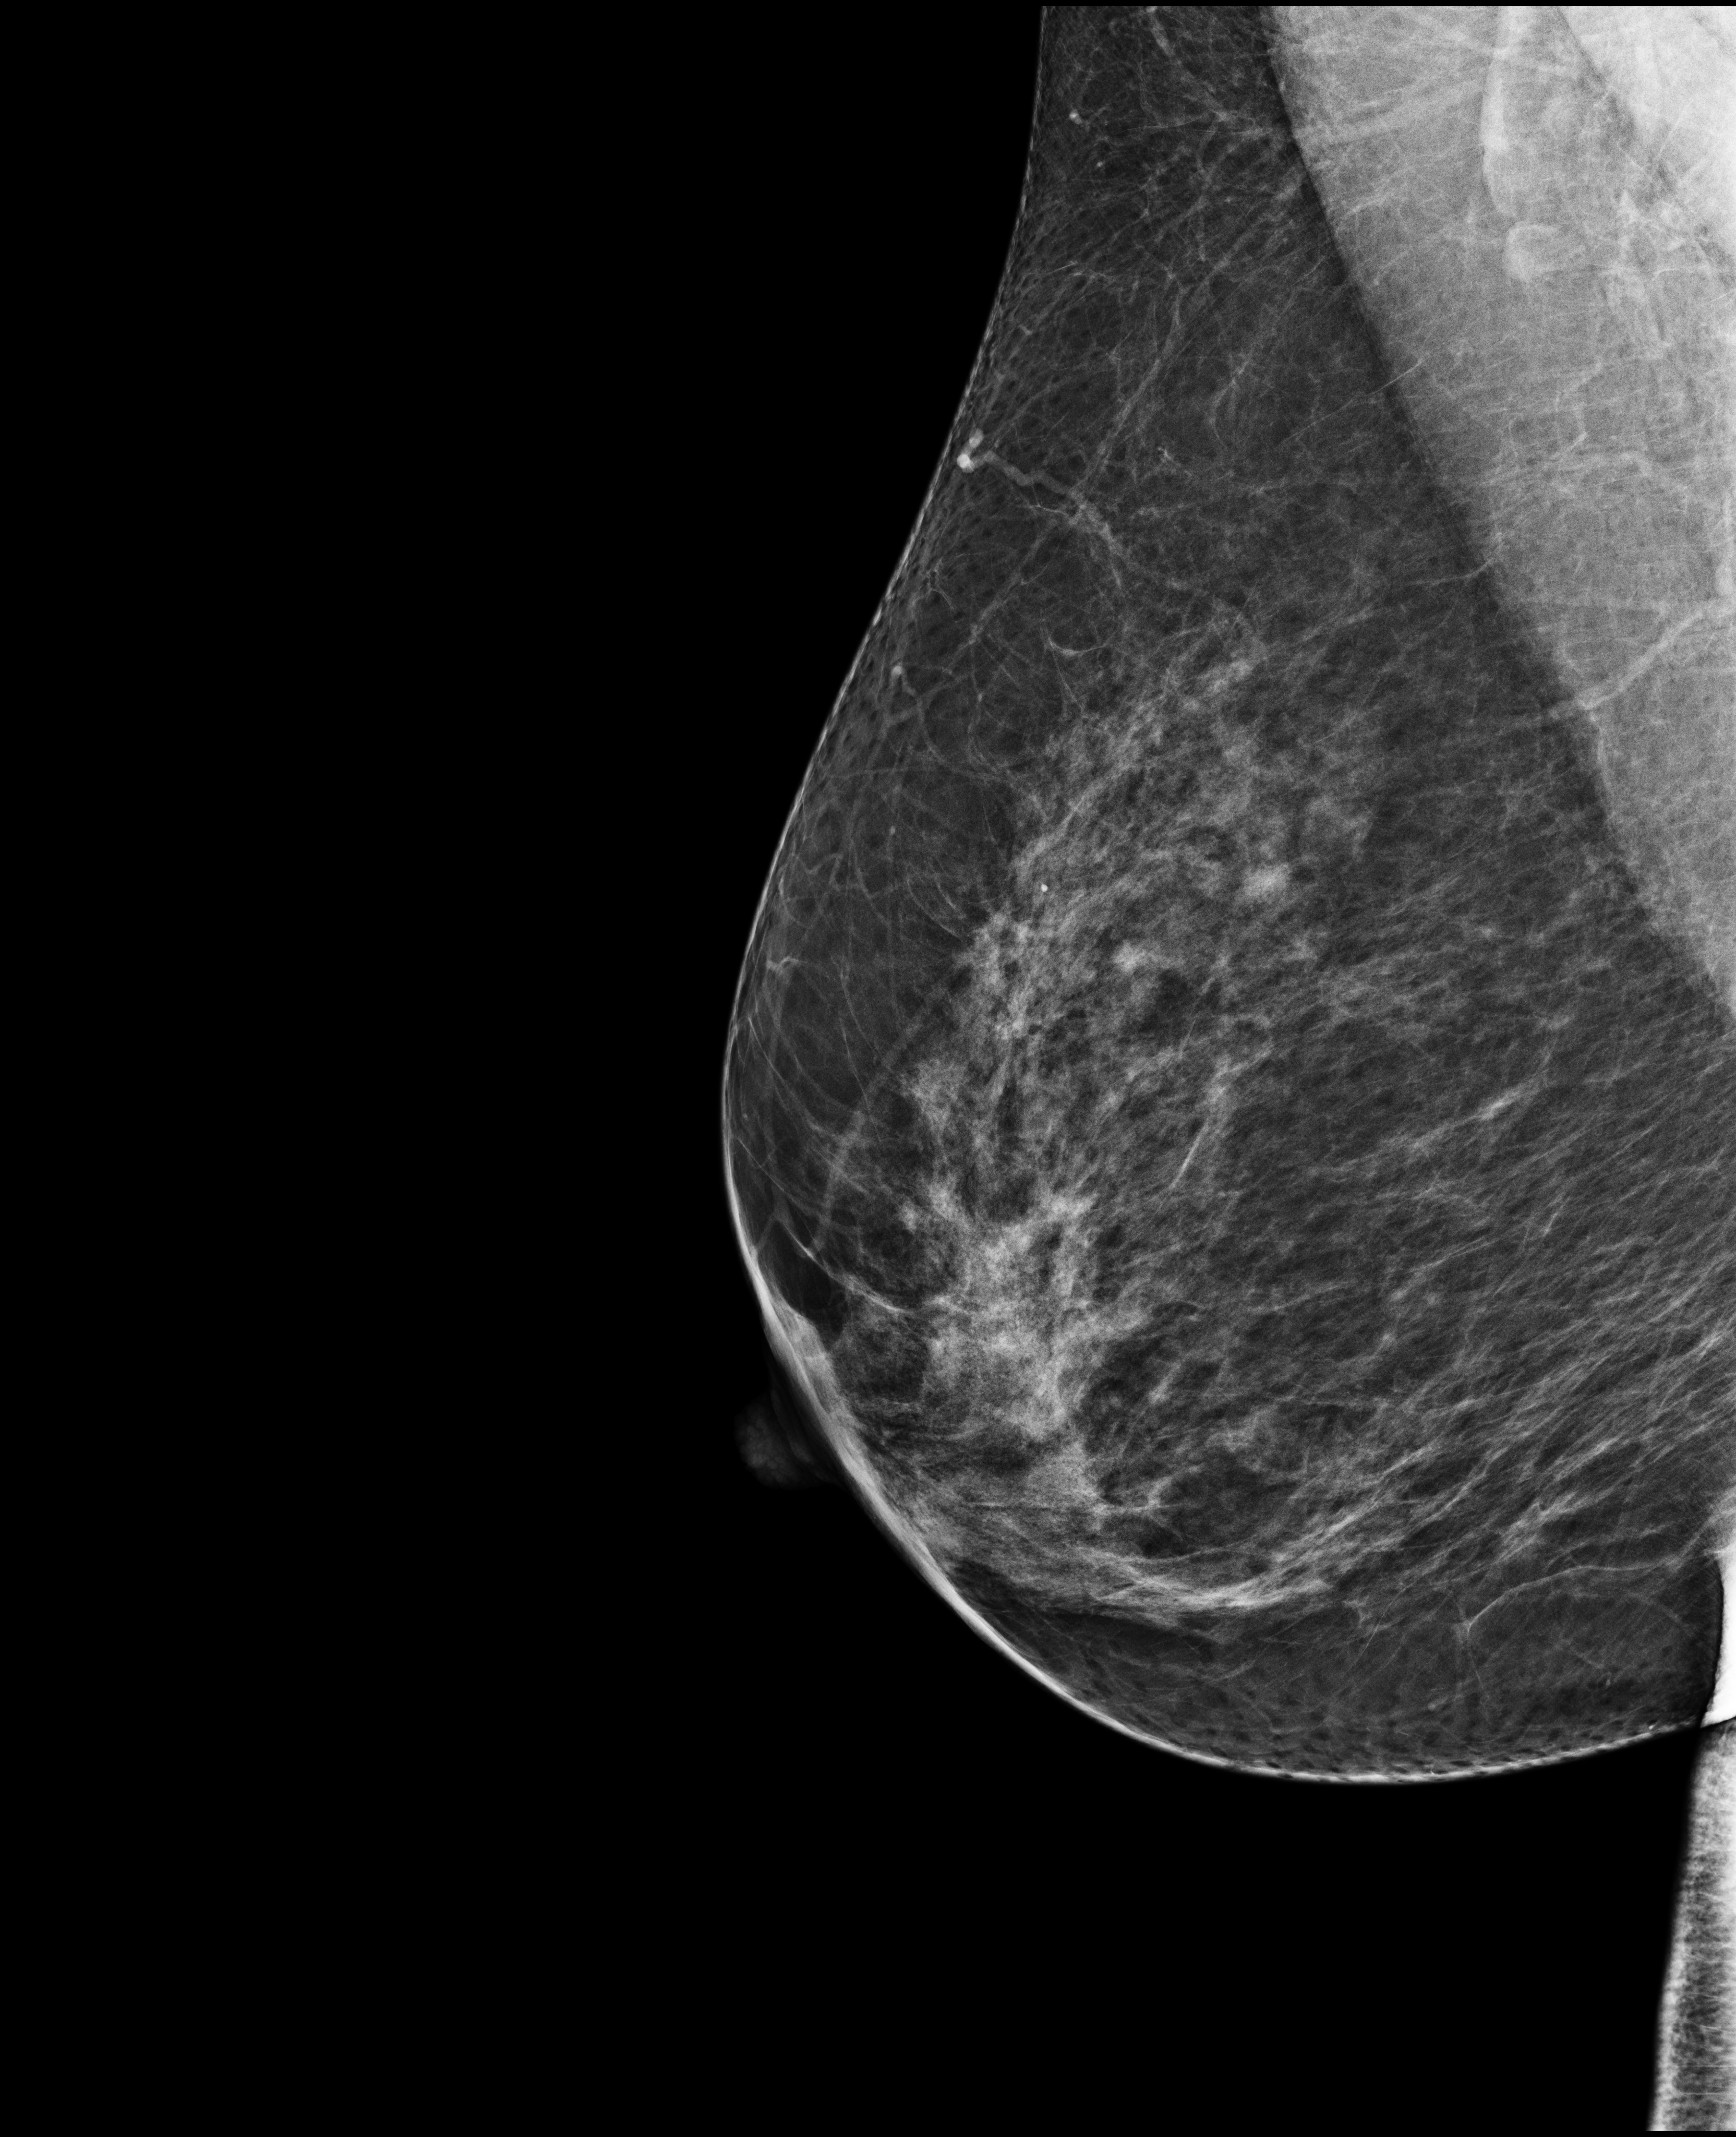
Full-field digital mammogram (FFDM); right breast; MLO view; screening examination; compressed breast thickness 77 mm. Female patient, age 47 years.
- breast density at the screening exam (both breasts): heterogeneously dense (BI-RADS density category c)
- final BI-RADS assessment for this screening round (tomosynthesis exam, both breasts): category 4
- recall: recalled for additional imaging after this screen